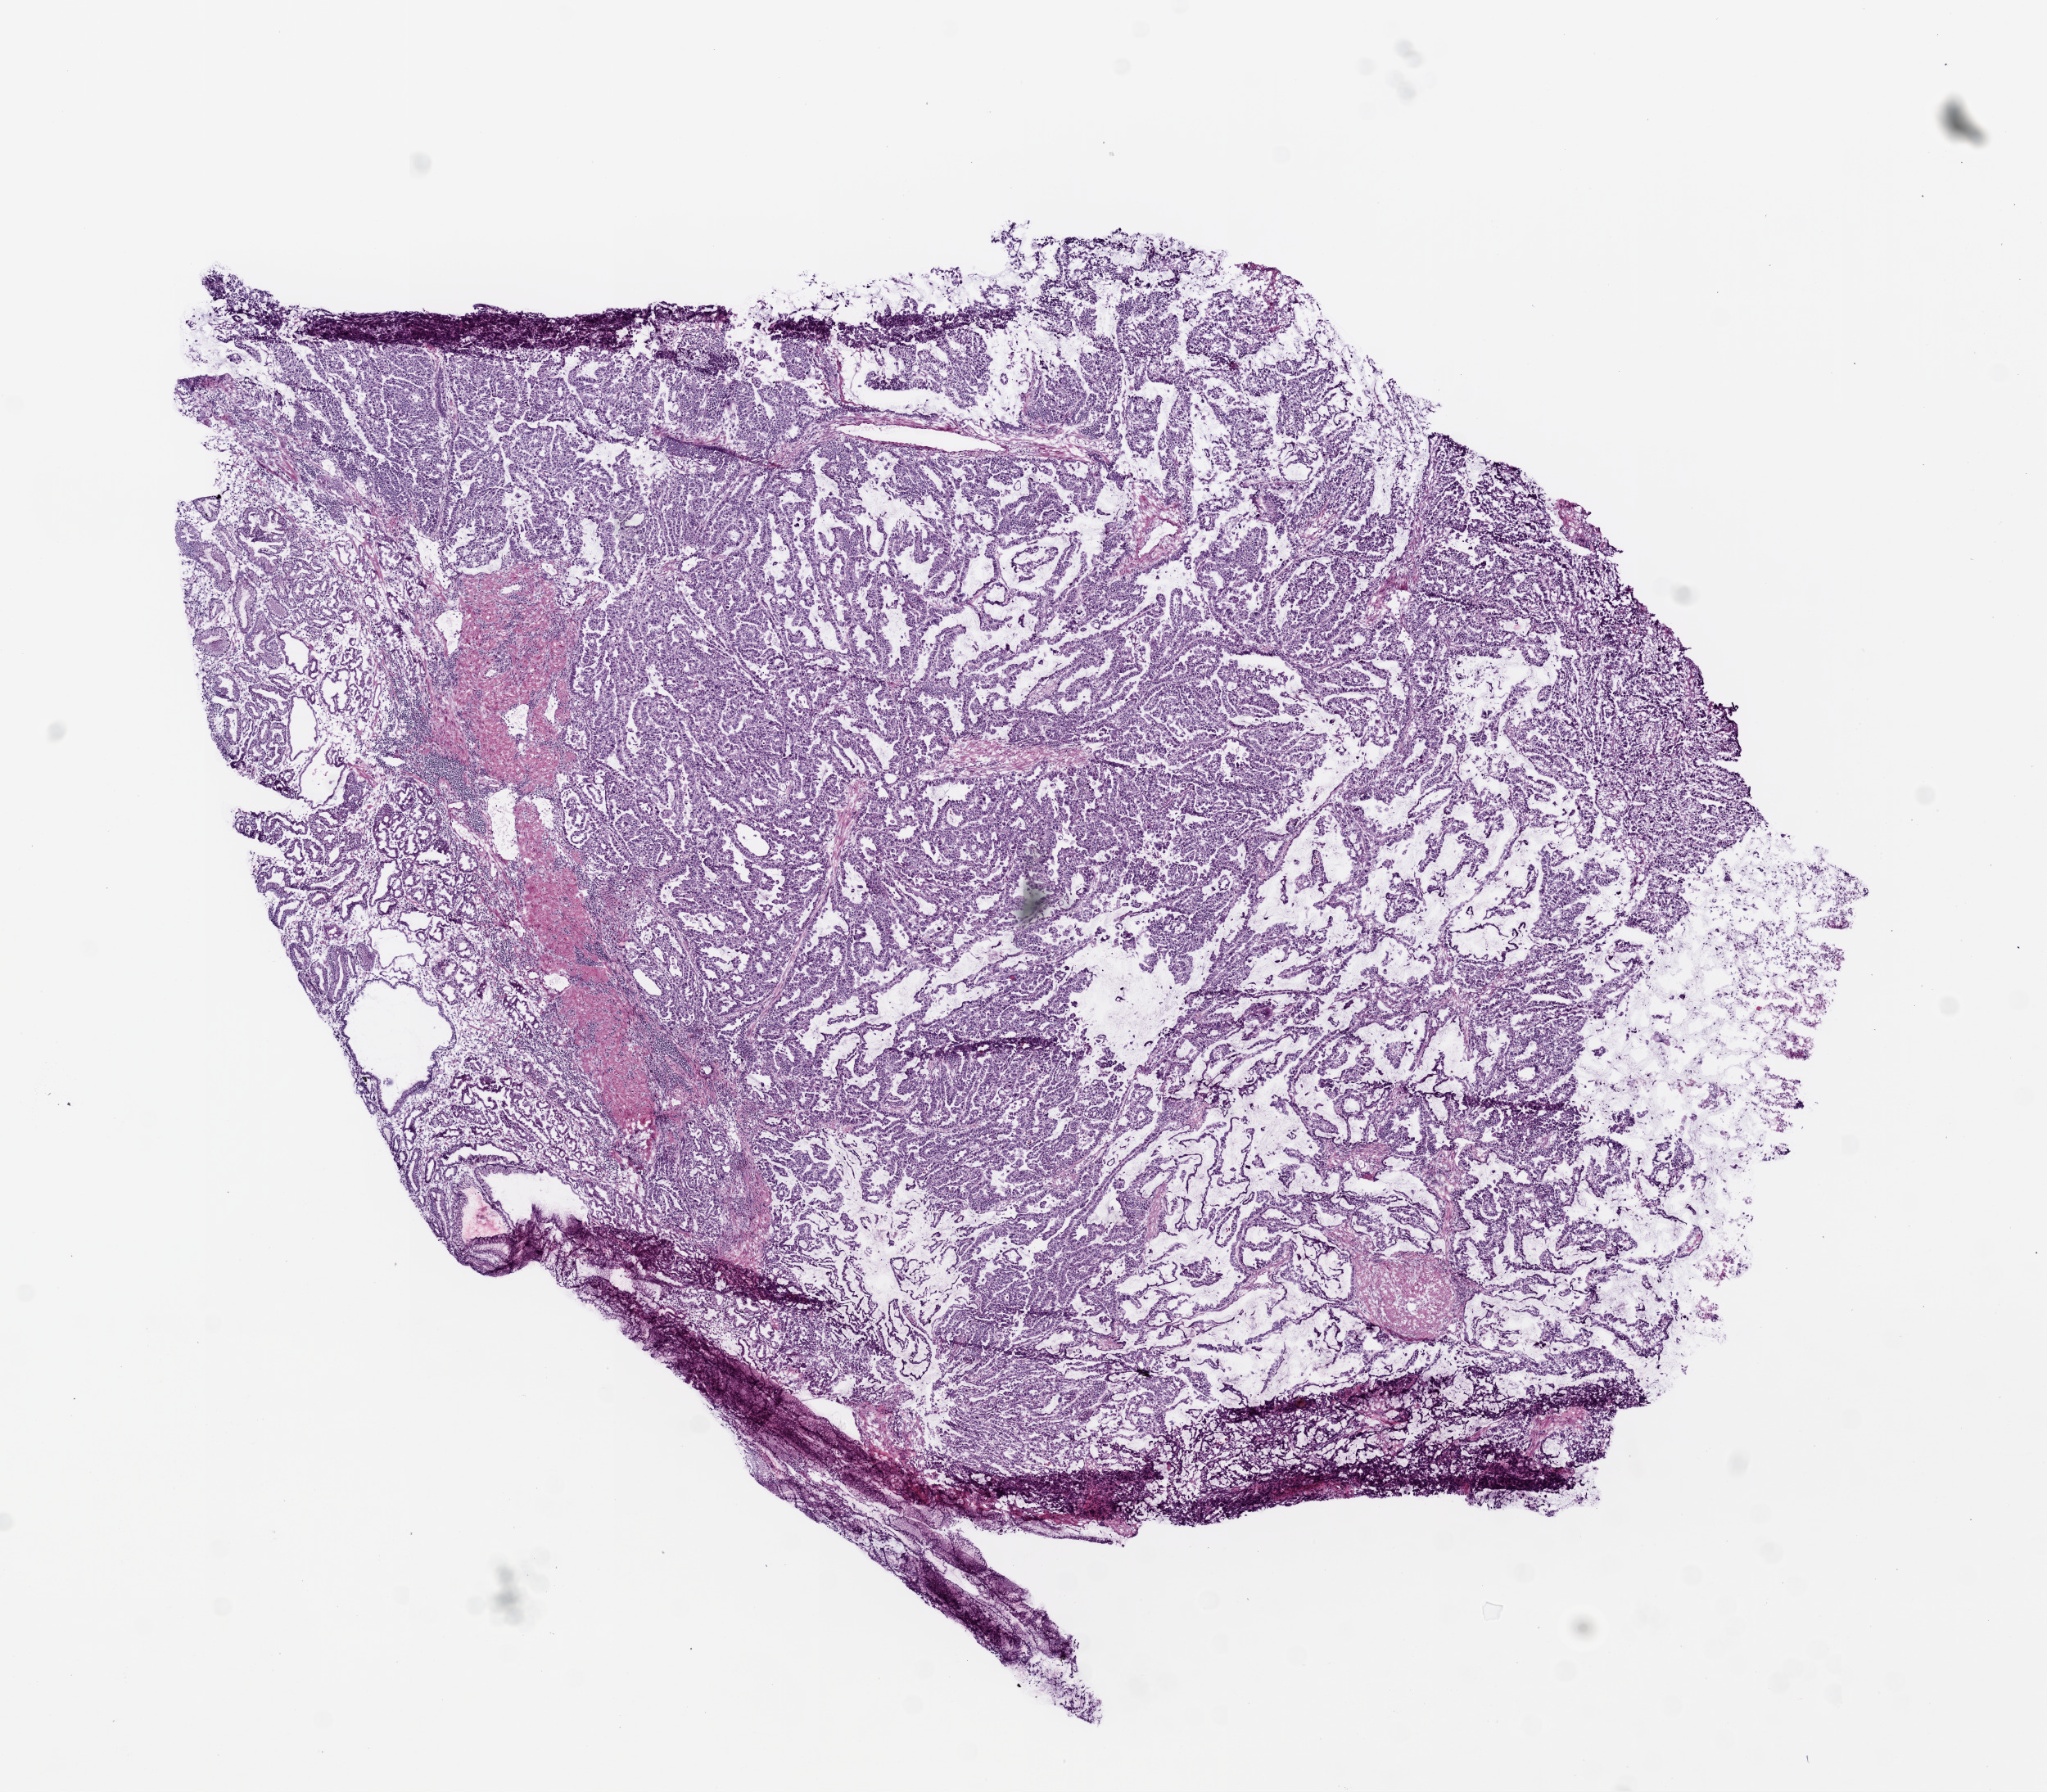
Digitized H&E-stained tissue section (whole slide), low-resolution overview of the scanned area, about 10.0 x 8.8 mm, frozen section, stomach, primary tumour sample. Female patient; age at initial diagnosis 66 years. Histologic grade: G2 (moderately differentiated). Slide review estimates, as recorded: tumour cells 75%, tumour nuclei 80%, normal cells 5%, stromal cells 10%, necrosis 10%.
* lymph nodes positive (case pathology): 2 of 33 examined
* AJCC pathologic stage: IV (6th edition)
* pathologic diagnosis: Adenocarcinoma, intestinal type (body of stomach)